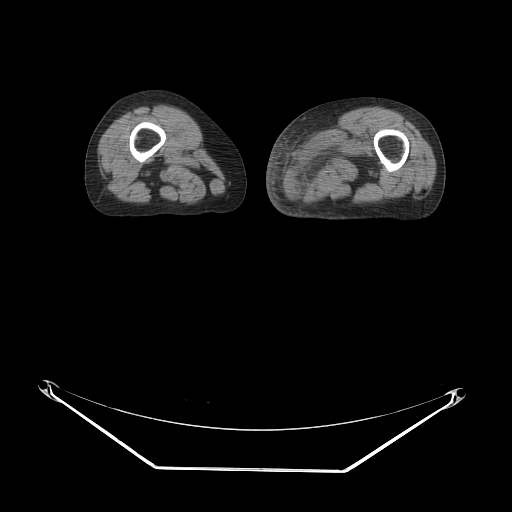
CT of an extremity soft-tissue mass (from a PET/CT study), one axial slice; slice 15 of 91 in the series (ordered by position); soft-tissue window (W 400 / L 40 HU); 512 × 512 image matrix, field of view 500 × 500 mm. Female patient. From the clinical record (not read from this slice): histological type: pleomorphic leiomyosarcoma; grade: high; site of the primary tumour: left thigh.
Structures marked on this image (expert contour drawn on MRI and transferred to this co-registered scan by the dataset authors):
- gross tumour volume including surrounding oedema: bounding box <288,128,376,197> (left, top, right, bottom; pixels)
- gross tumour volume (mass): <290,165,320,197>